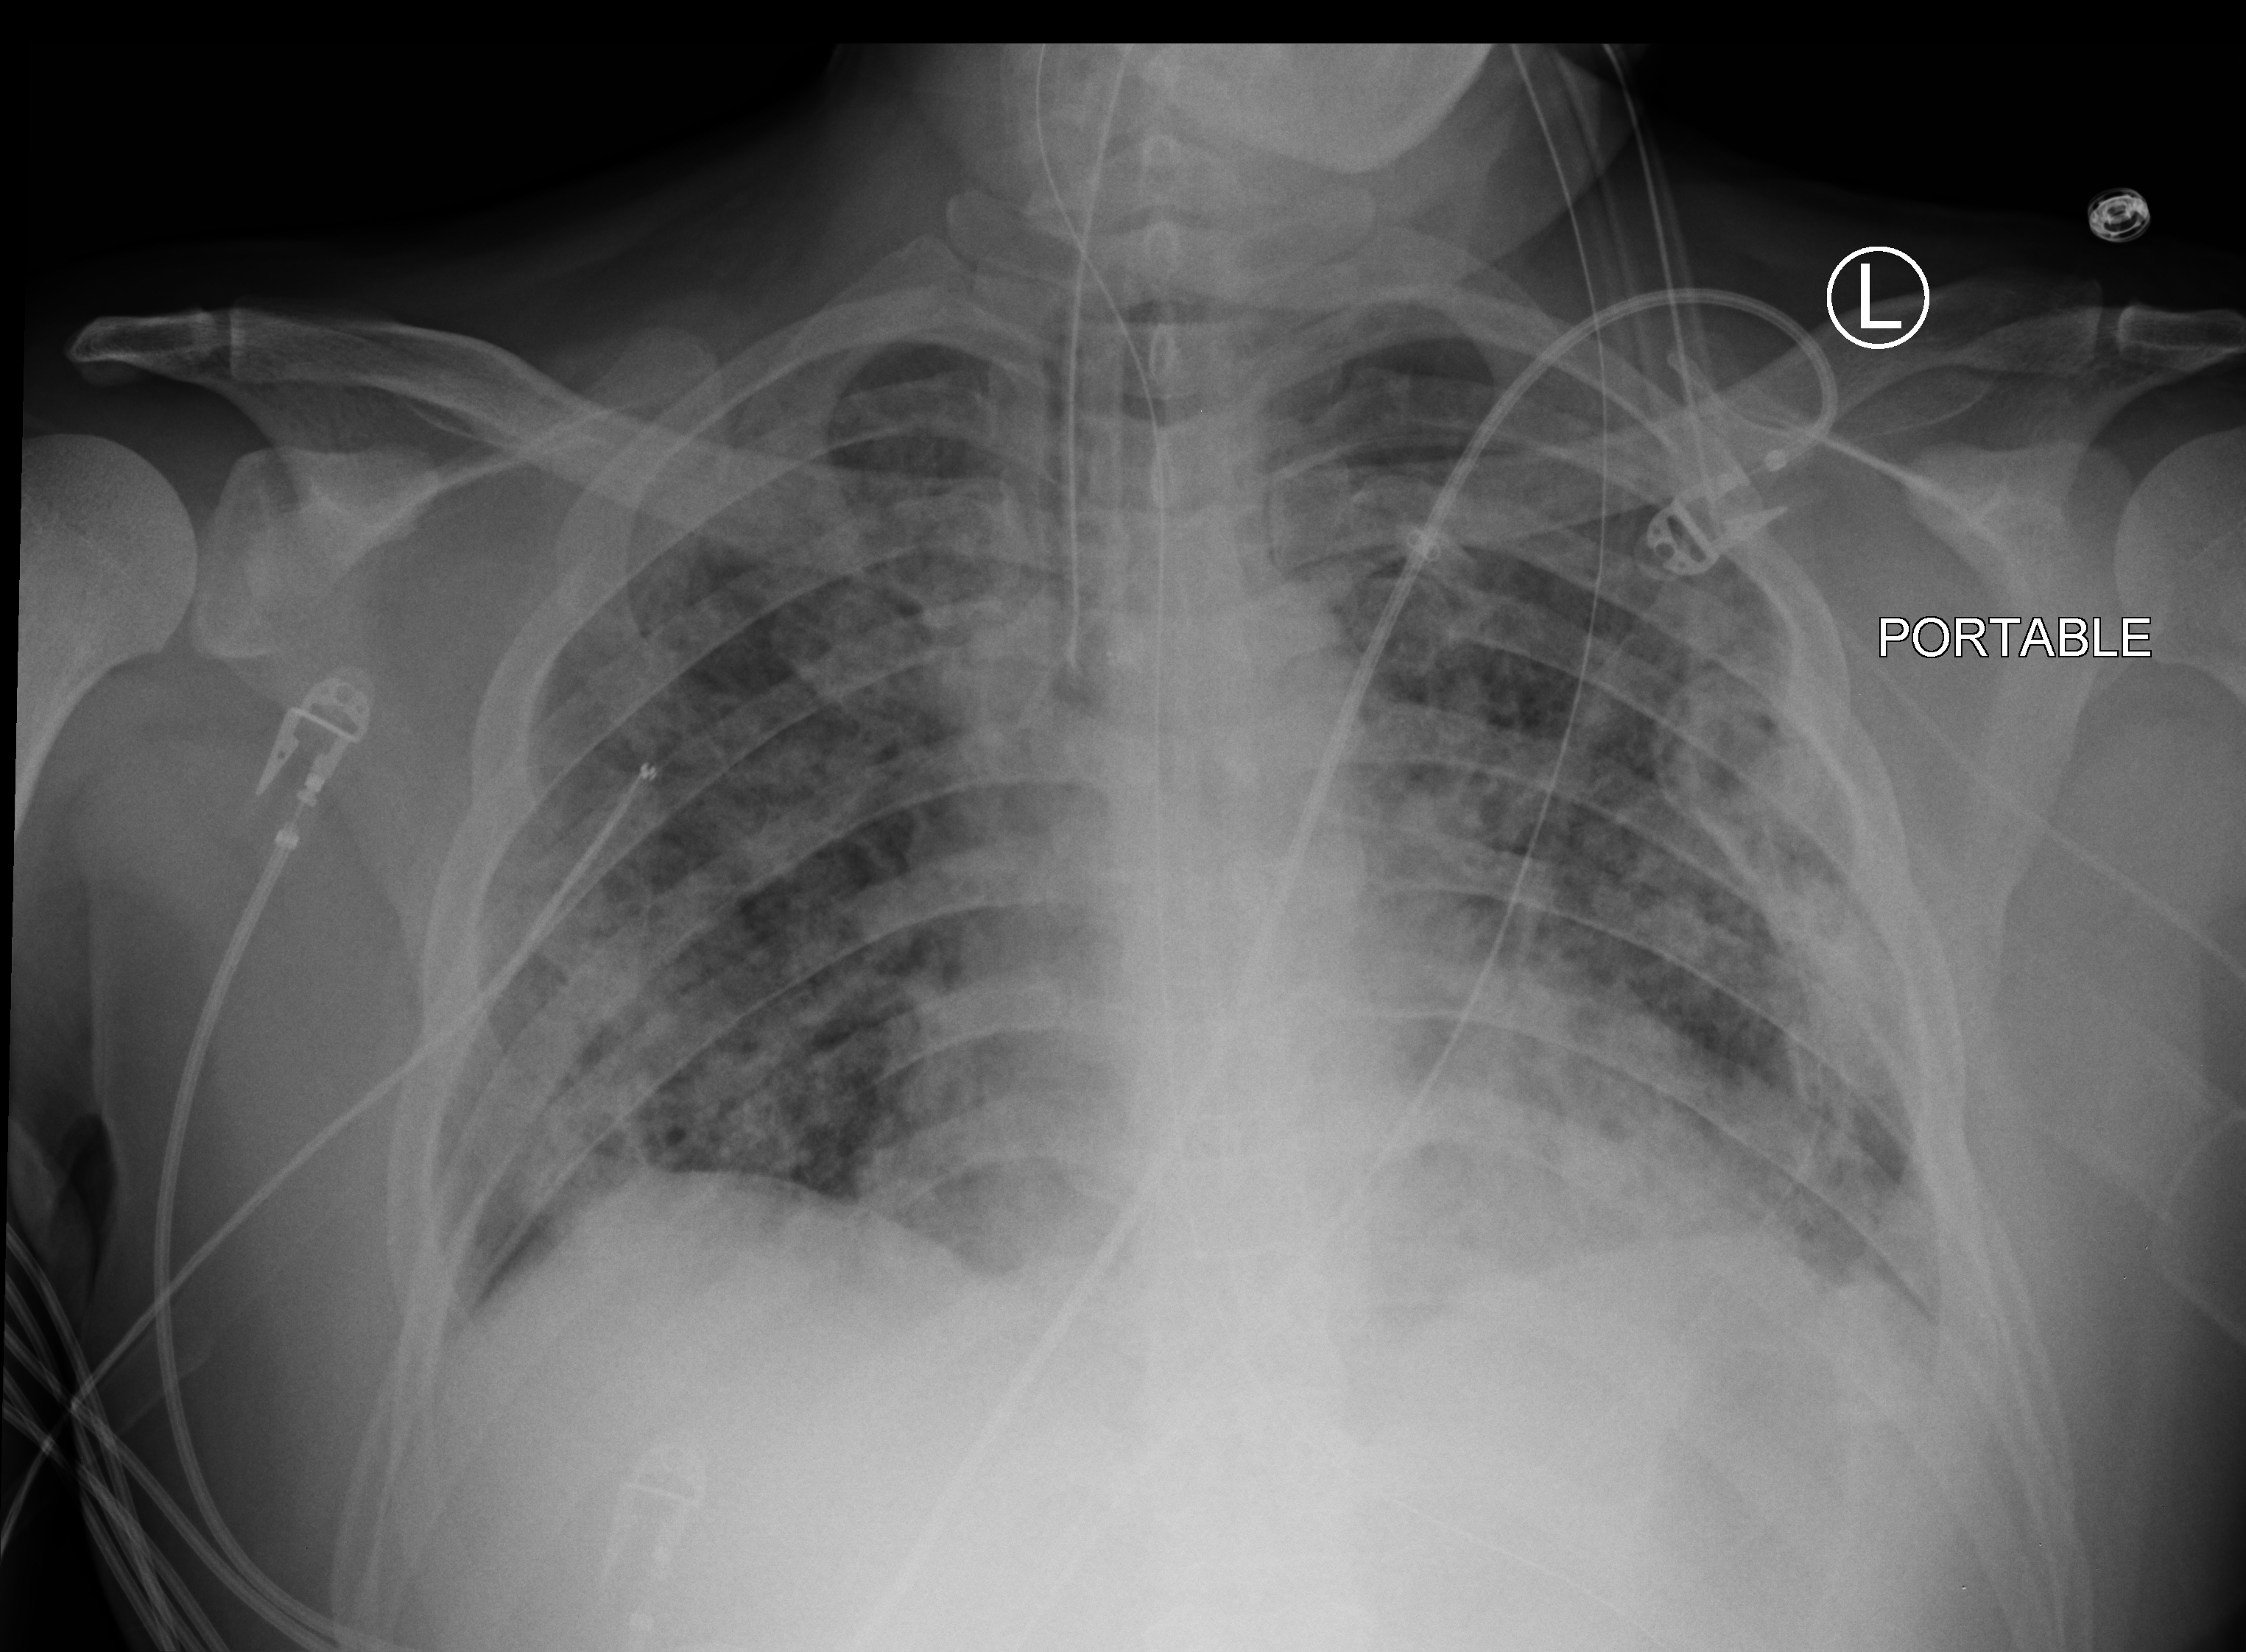
Portable chest radiograph, anteroposterior (AP) projection. Patient hospitalised with COVID-19; male, aged 18–59 years.
From the hospital-stay record, not from the radiograph (when in the stay this image was taken is not recorded): other chronic lung disease (admission record): no; mechanically ventilated during this hospital stay: yes.